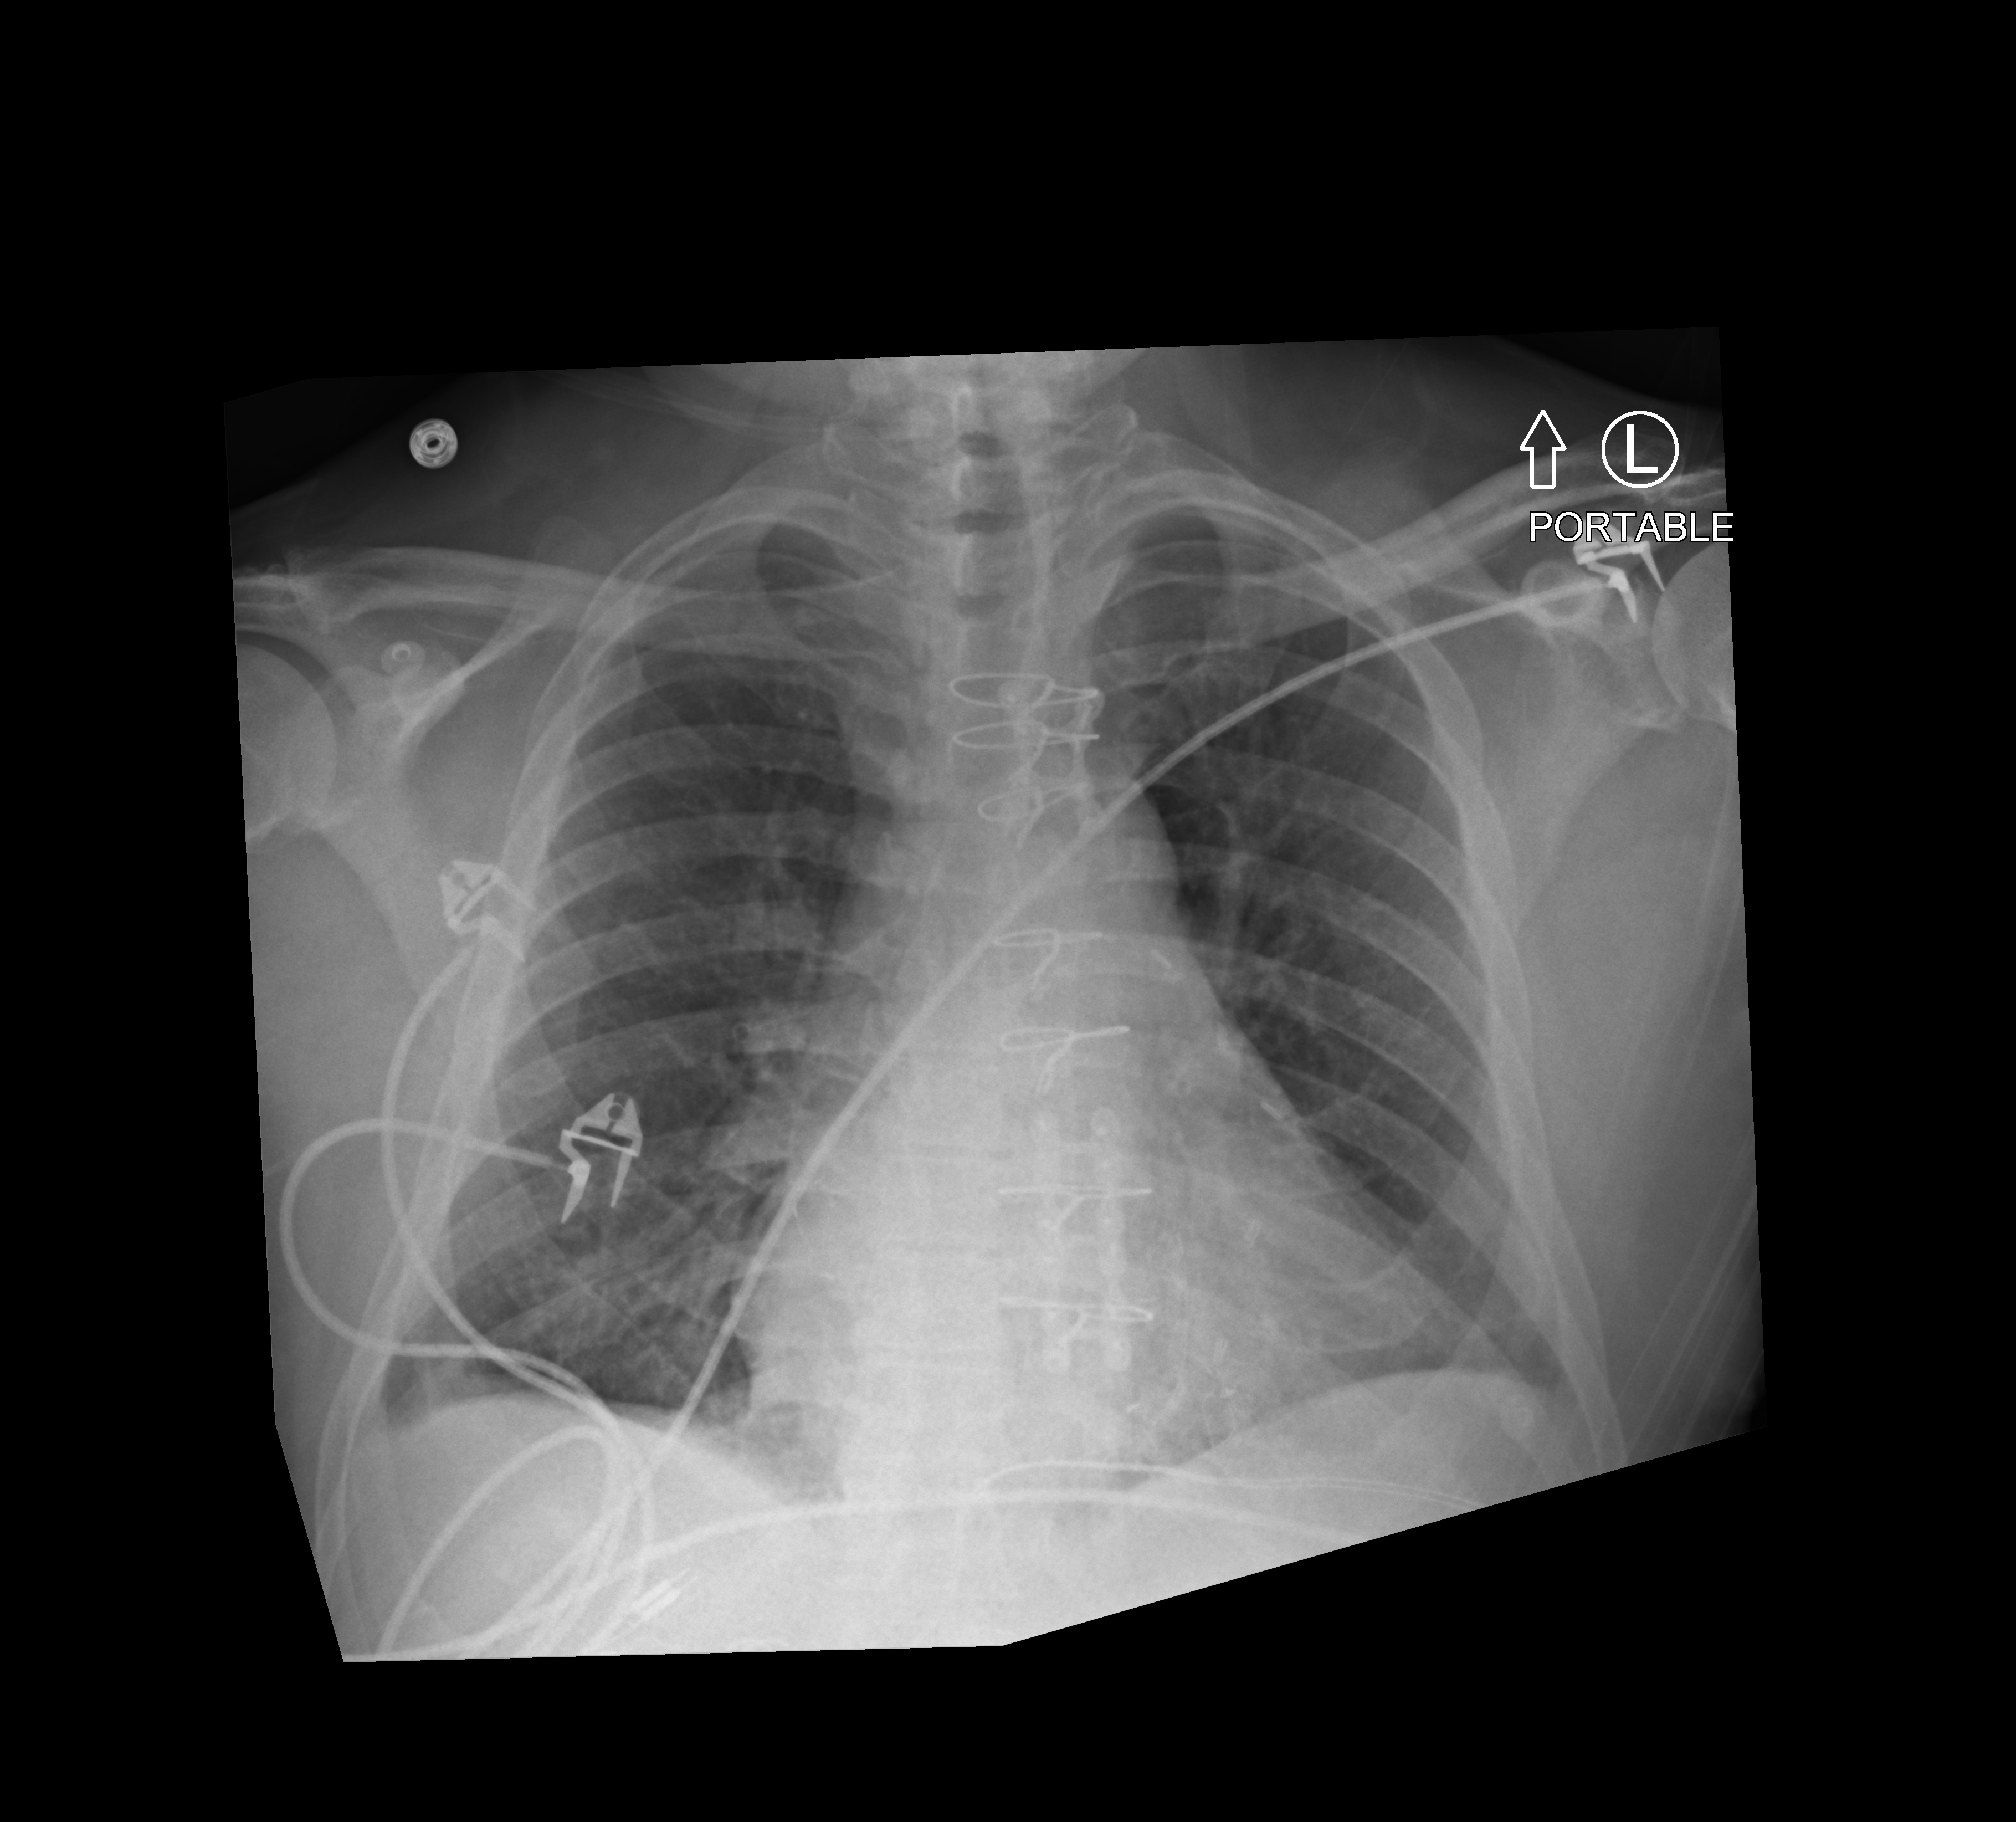
Chest X-ray (portable); anteroposterior (AP) projection. Patient hospitalised with COVID-19; male, aged 60–74 years.
Hospital-stay facts (about this admission, not read from this image; timing relative to this image not recorded):
- length of hospital stay: 4 days
- diabetes (admission record): yes
- mechanically ventilated during this hospital stay: no